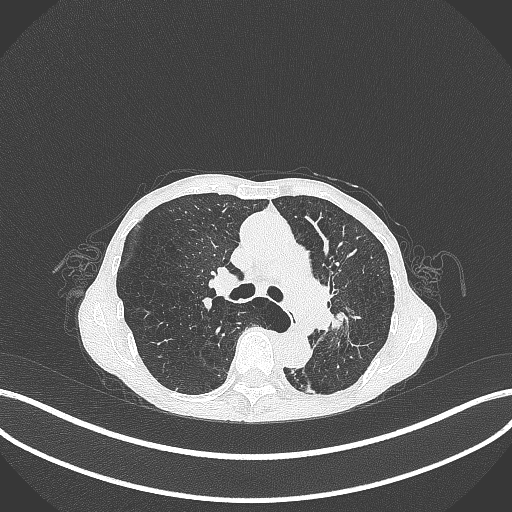
Chest CT, one axial slice; slice 177 of 347 in the series (ordered by position); reconstruction kernel B70f; lung window (W 1500 / L -600 HU); 512 × 512 image matrix. Female patient, age 70 years. From the clinical record (not read from this slice): clinical TNM (as recorded): T3 N0 M0; histopathological grade: G3.
Annotated regions visible in this slice (bounding box drawn by a radiologist):
- lung tumour (recorded histology: small cell carcinoma): bounding box <331,303,358,339> (left, top, right, bottom; pixels)